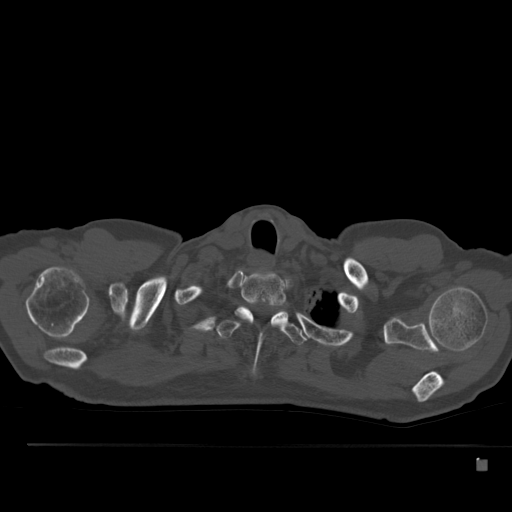
CT including the spine, one axial slice; slice 420 of 517 in the series (ordered by position); reconstruction kernel Br40s; 120 kVp; bone window (W 1800 / L 400 HU); 1.5 mm slice thickness; 512 × 512 image matrix. Male patient, age 70 years. From the clinical record (not read from this slice): primary cancer: renal; vertebrae with lytic lesions (as recorded): T4, T6, T10, T12, L3, L4, L5.
Outlined on this slice (semi-automatic segmentation, software-assisted and operator-edited):
- T1 vertebra: bounding box <238,271,286,325> (left, top, right, bottom; pixels)
- T2 vertebra: <217,305,308,376>